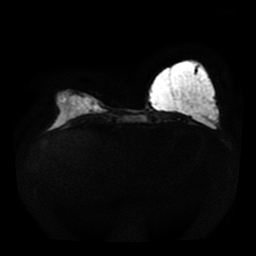
Breast MRI, one axial slice. Position 14 of 41 along the scan axis. Diffusion-weighted series; image 2 of 4 stored at this slice position (different b-values; order by instance number). 1.5 T. 5 mm slice thickness. 256 × 256 image matrix. Female patient.
Structures marked on this image (manually delineated by an expert):
- tumour on diffusion-weighted imaging: bounding box (x1, y1, x2, y2) in pixels: (81, 97, 98, 110)